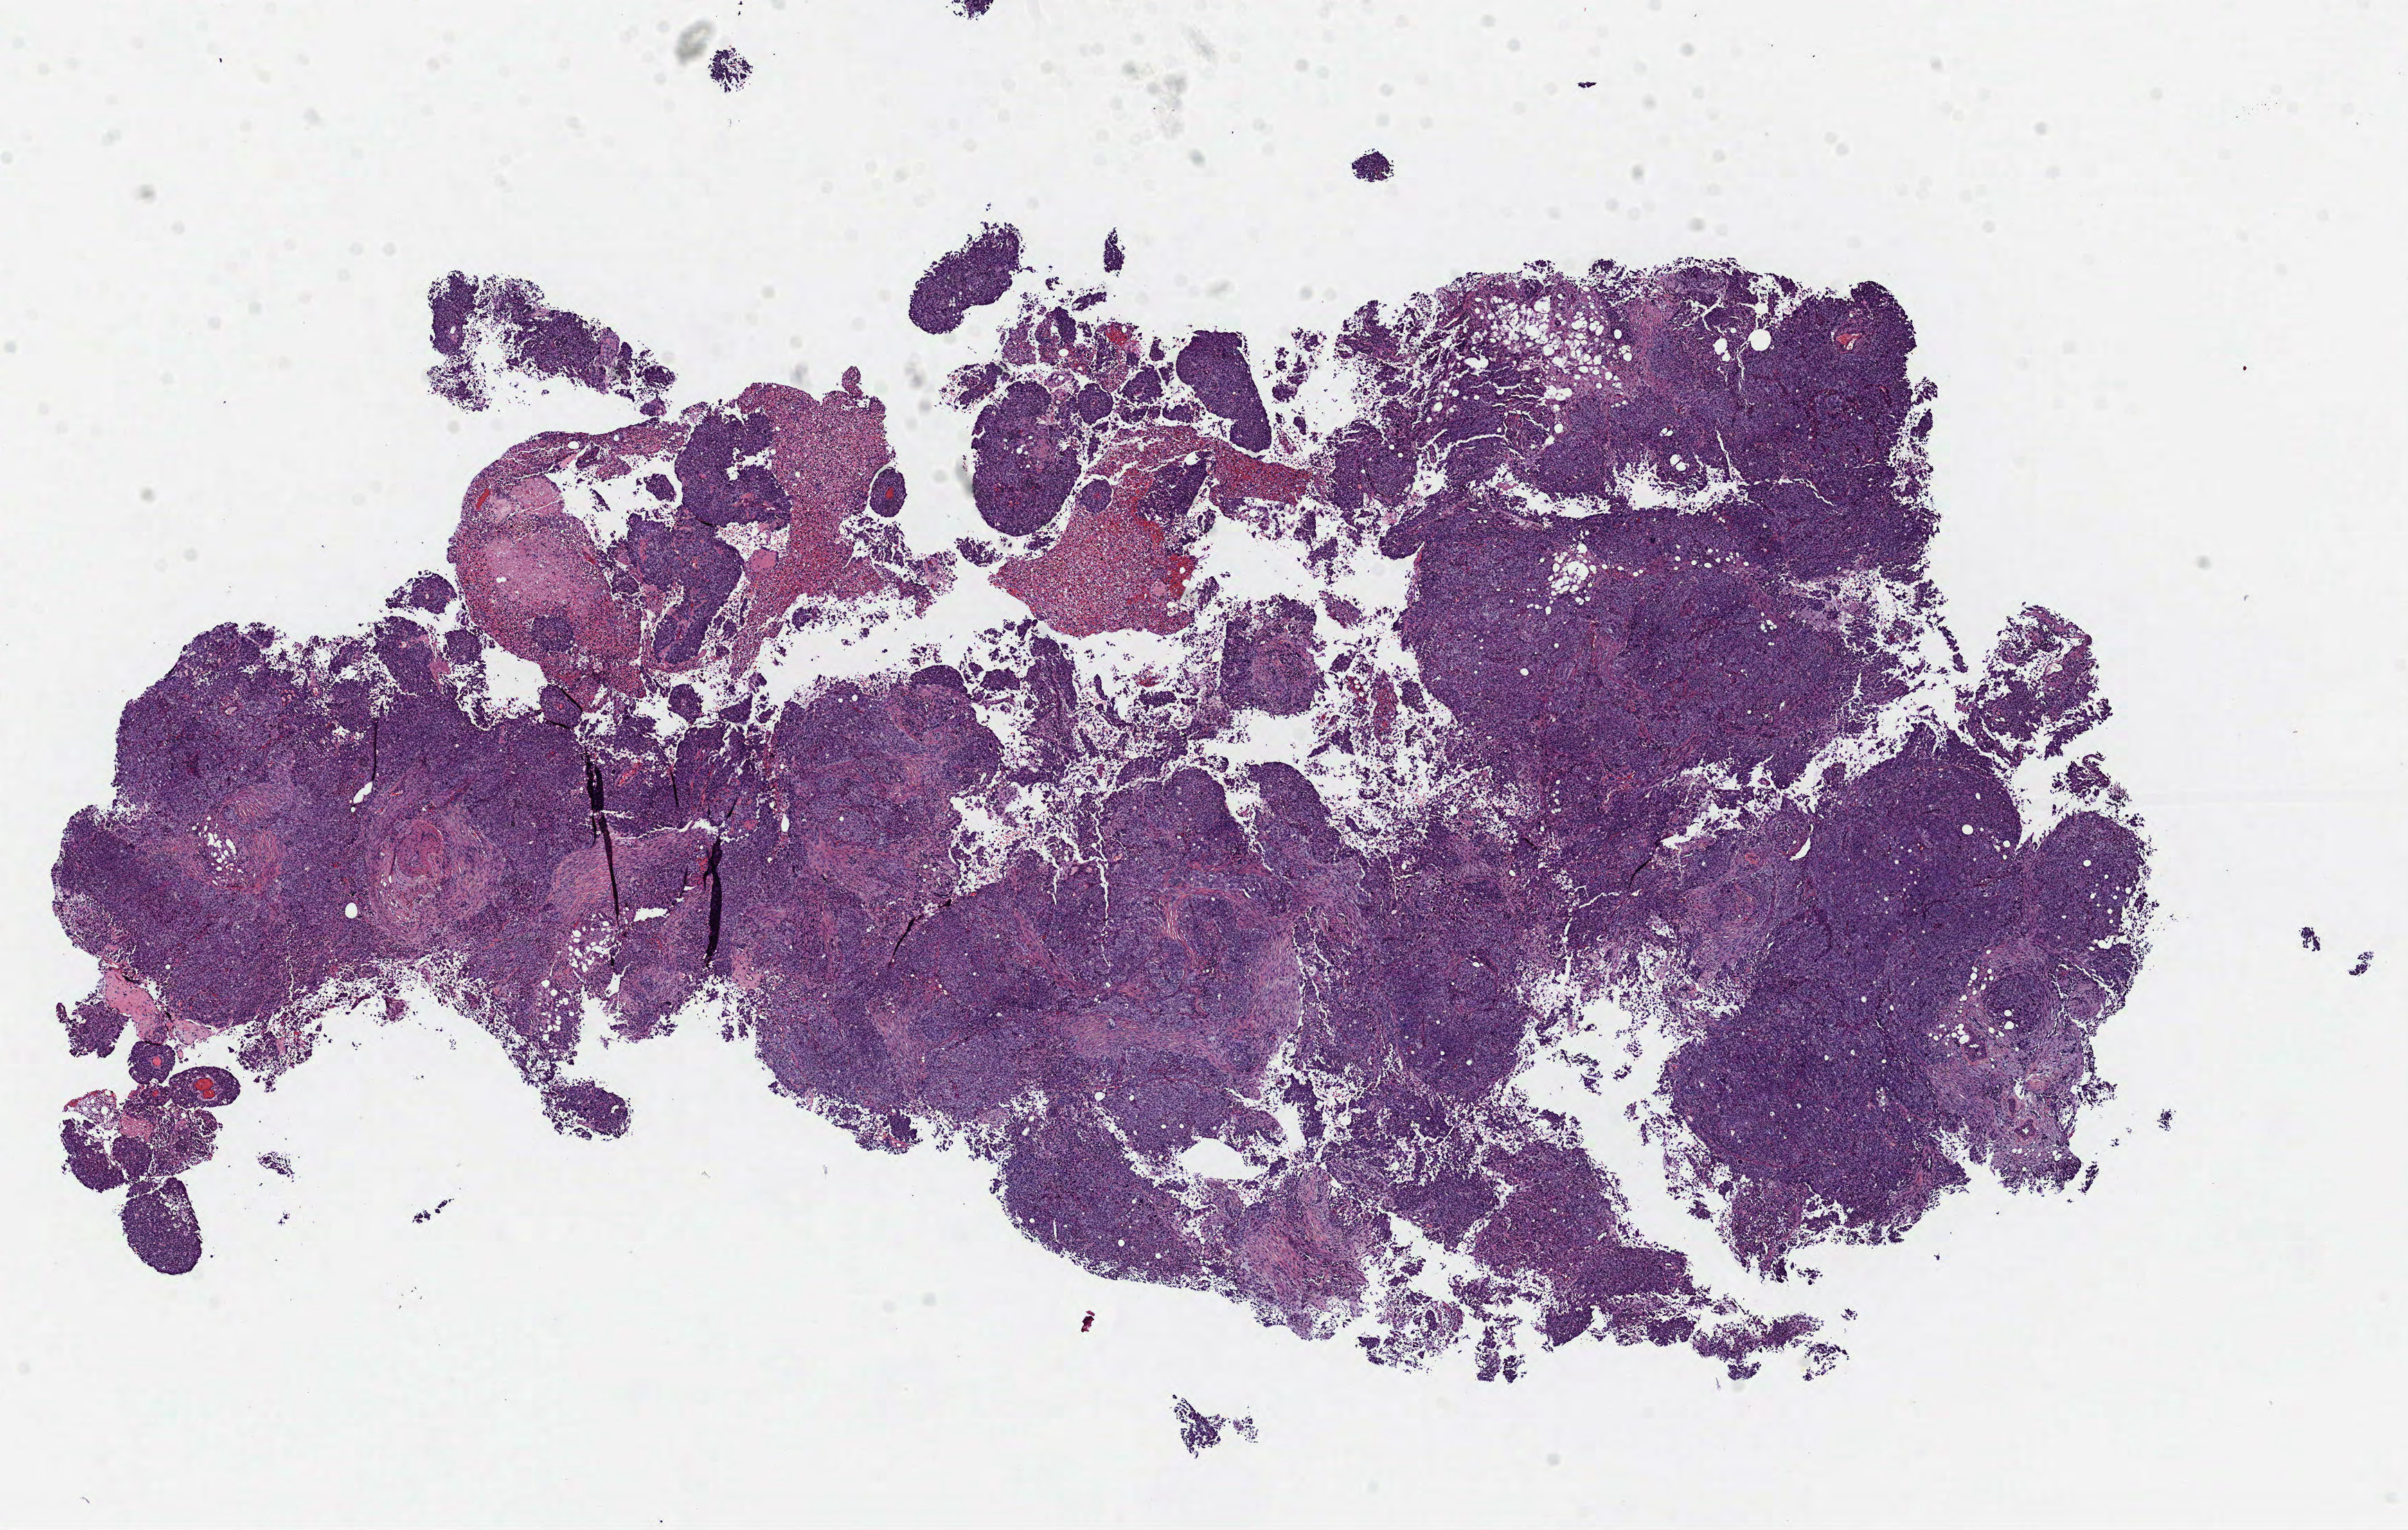
Hematoxylin and eosin (H&E) stained whole-slide image — low-resolution overview of the scanned area, about 14.0 x 8.9 mm; formalin-fixed paraffin-embedded (FFPE) diagnostic section; primary tumour sample from the ovary. Female, age 75 years at initial diagnosis.
Histologic diagnosis: Serous cystadenocarcinoma, NOS.